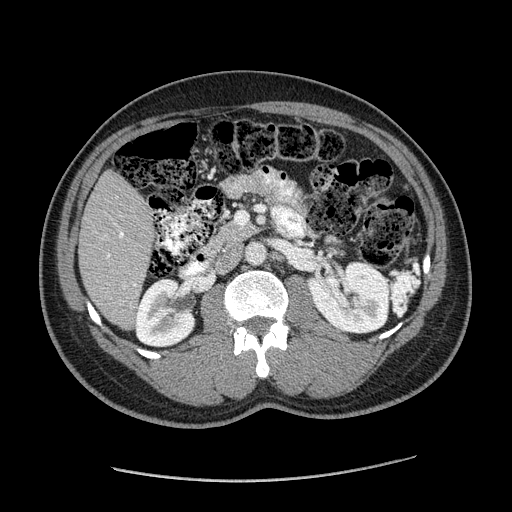
Contrast-enhanced abdominal CT (liver protocol), one axial slice. Position 65 of 182 along the scan axis. Reconstruction kernel STANDARD. 120 kVp. Soft-tissue window (W 400 / L 40 HU). 512 × 512 image matrix. Case-level facts recorded for this patient, not image findings: diagnosis: hepatocellular carcinoma (patient treated with transarterial chemoembolisation; whether this scan precedes or follows treatment is not stated here); TNM stage (as recorded): Stage-I; Child-Pugh class: A; tumour differentiation: well differentiated; tumour nodularity: uninodular.
Outlined on this slice (semi-automatic segmentation, software-assisted and operator-edited):
- liver parenchyma outside the tumour (the mass and vessels are separate outlines, so this box may not span the whole liver): bounding box [x1, y1, x2, y2] px = [78, 170, 154, 328]
- liver vessels: [107, 232, 136, 286]